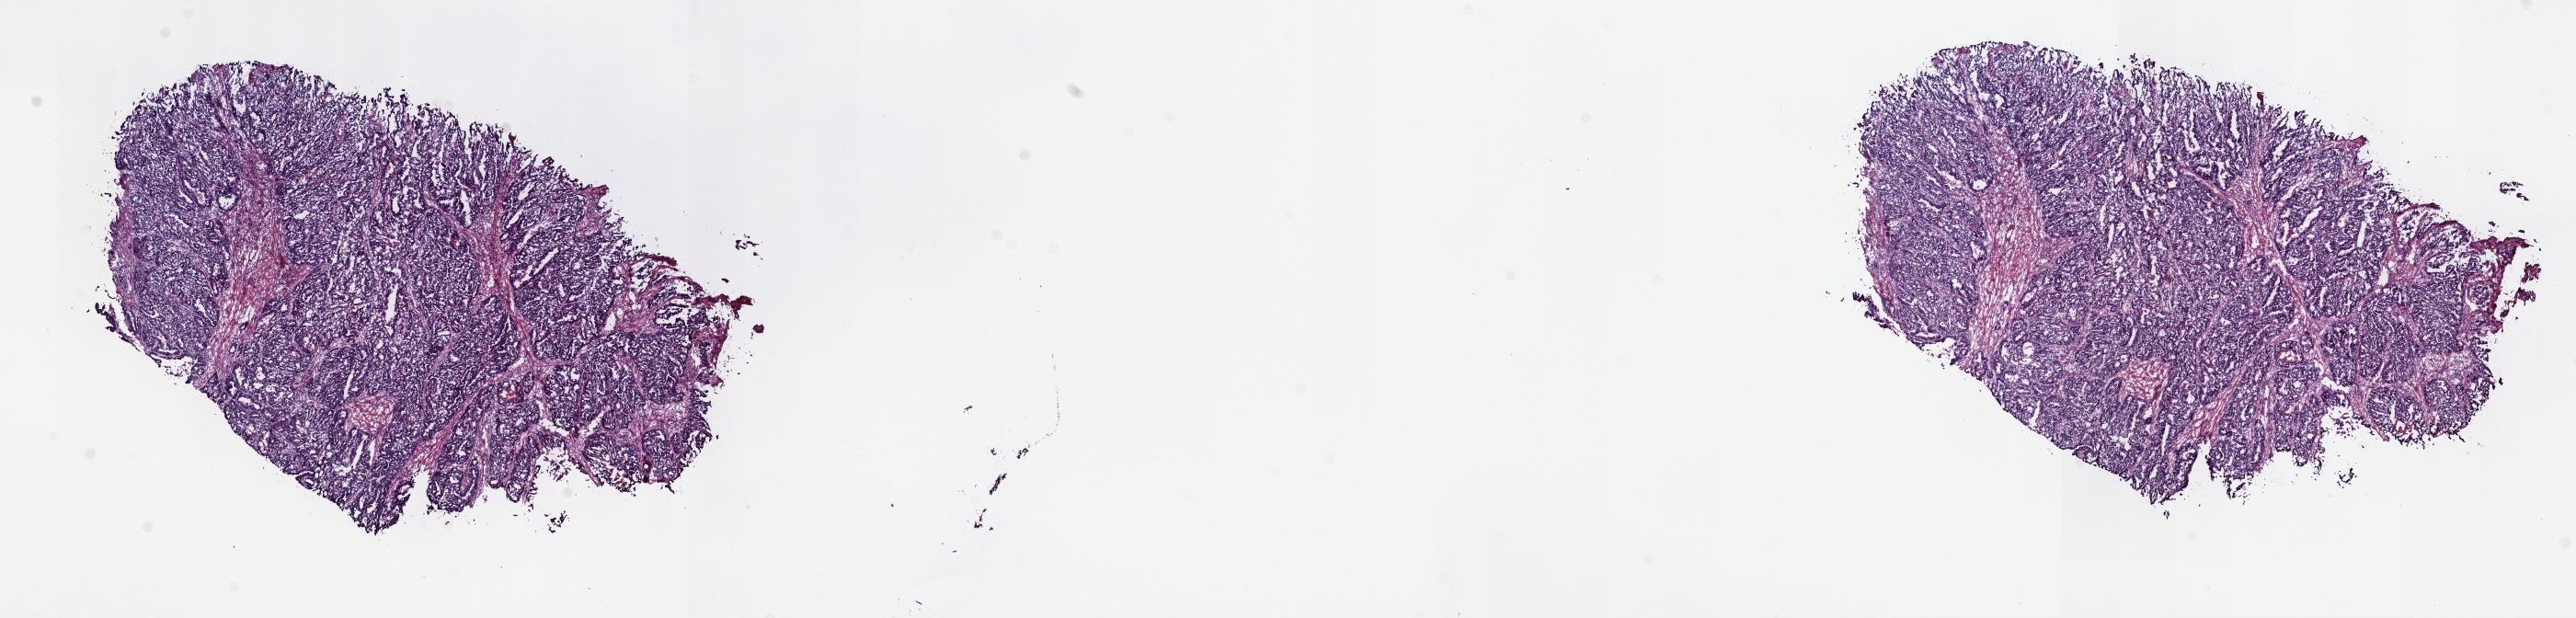
Whole-slide histology image, Hematoxylin and eosin (H&E) stained — shown as a low-resolution overview of the whole scanned area (about 22.7 x 5.4 mm). Frozen section. Stomach, primary tumour sample. Female, age 67 years at initial diagnosis. Histologic grade: G2 (moderately differentiated). Pathologist review of this section (percent, as recorded): tumour cells 100%, tumour nuclei 75%, normal cells 0%, stromal cells 0%, necrosis 0%. Inflammatory infiltration, as recorded: lymphocyte infiltration 4%, monocyte infiltration 0%, neutrophil infiltration 0%.
AJCC pathologic stage: IIIA (6th edition). Diagnosis: Tubular adenocarcinoma (gastric antrum). Lymph nodes positive (case pathology): 2 of 19 examined.